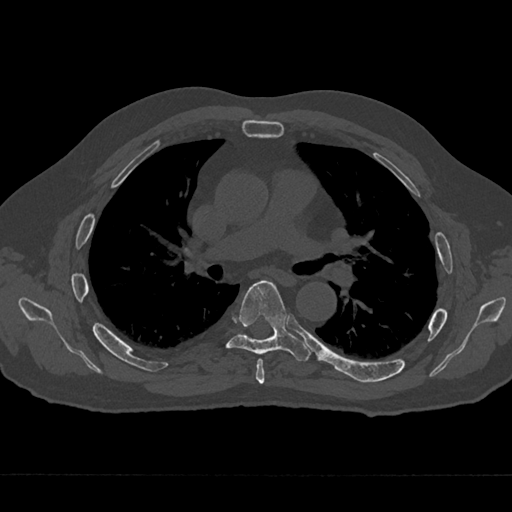
CT including the spine, one axial slice. Position 429 of 797 along the scan axis. Bone window (W 1800 / L 400 HU). 512 × 512 image matrix. Male patient, age 75 years. Case-level facts recorded for this patient, not image findings: primary cancer: renal; vertebrae with lytic lesions (as recorded): T4.
Outlined on this slice (semi-automatically segmented with operator editing):
- T5 vertebra: bounding box (x1, y1, x2, y2) in pixels: (256, 359, 265, 384)
- T6 vertebra: (225, 280, 310, 361)